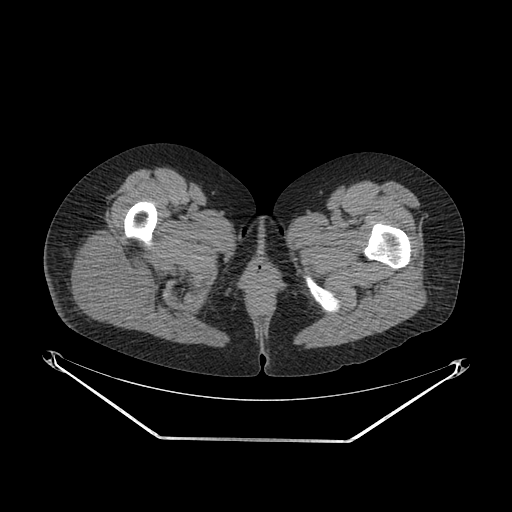
CT of an extremity soft-tissue mass (from a PET/CT study), one axial slice; position 31 of 267 along the scan axis; reconstruction kernel SOFT; soft-tissue window (W 400 / L 40 HU); 512 × 512 image matrix, field of view 500 × 500 mm. Female patient. Case-level facts recorded for this patient, not image findings: histological type: epithelioid sarcoma with vascular differentiation; site of the primary tumour: right buttock.
Outlined on this slice (expert contour drawn on MRI and transferred to this co-registered scan by the dataset authors):
- gross tumour volume (mass): box from (x=69, y=233) to (x=149, y=321) px